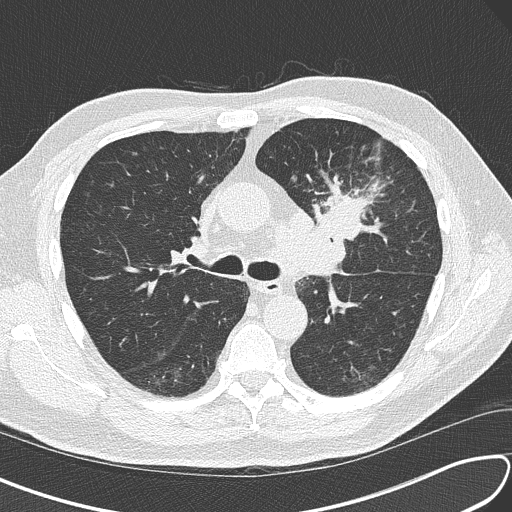
Axial slice from a low-dose chest CT screening exam; third annual screen; lung window (W 1500 / L -600 HU); 2 mm slice thickness; lung (sharp) reconstruction kernel (B50f); slice 58 of 156 in the series. Male participant, aged 67 years at enrolment. Current smoker at enrolment.
Expert-annotated lung lesion, bounding box <297,169,398,262> (left, top, right, bottom; pixels). Screening reader's record for this exam (one nodule recorded; not confirmed to be the boxed lesion): non-calcified nodule or mass ≥4 mm, left upper lobe, 30 × 23 mm, soft tissue attenuation, pre-existing on the prior screen: no.